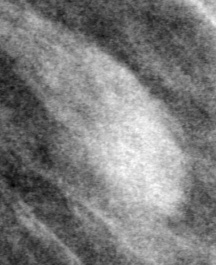
Region of interest cut from a scanned film mammogram (one marked finding), right breast, CC view, BI-RADS breast density category 4 (scale 1–4).
- Mass, shape oval, margins obscured; BI-RADS assessment category 3; subtlety rating 3 on a 1 (subtle) to 5 (obvious) scale; pathology (as recorded): benign.